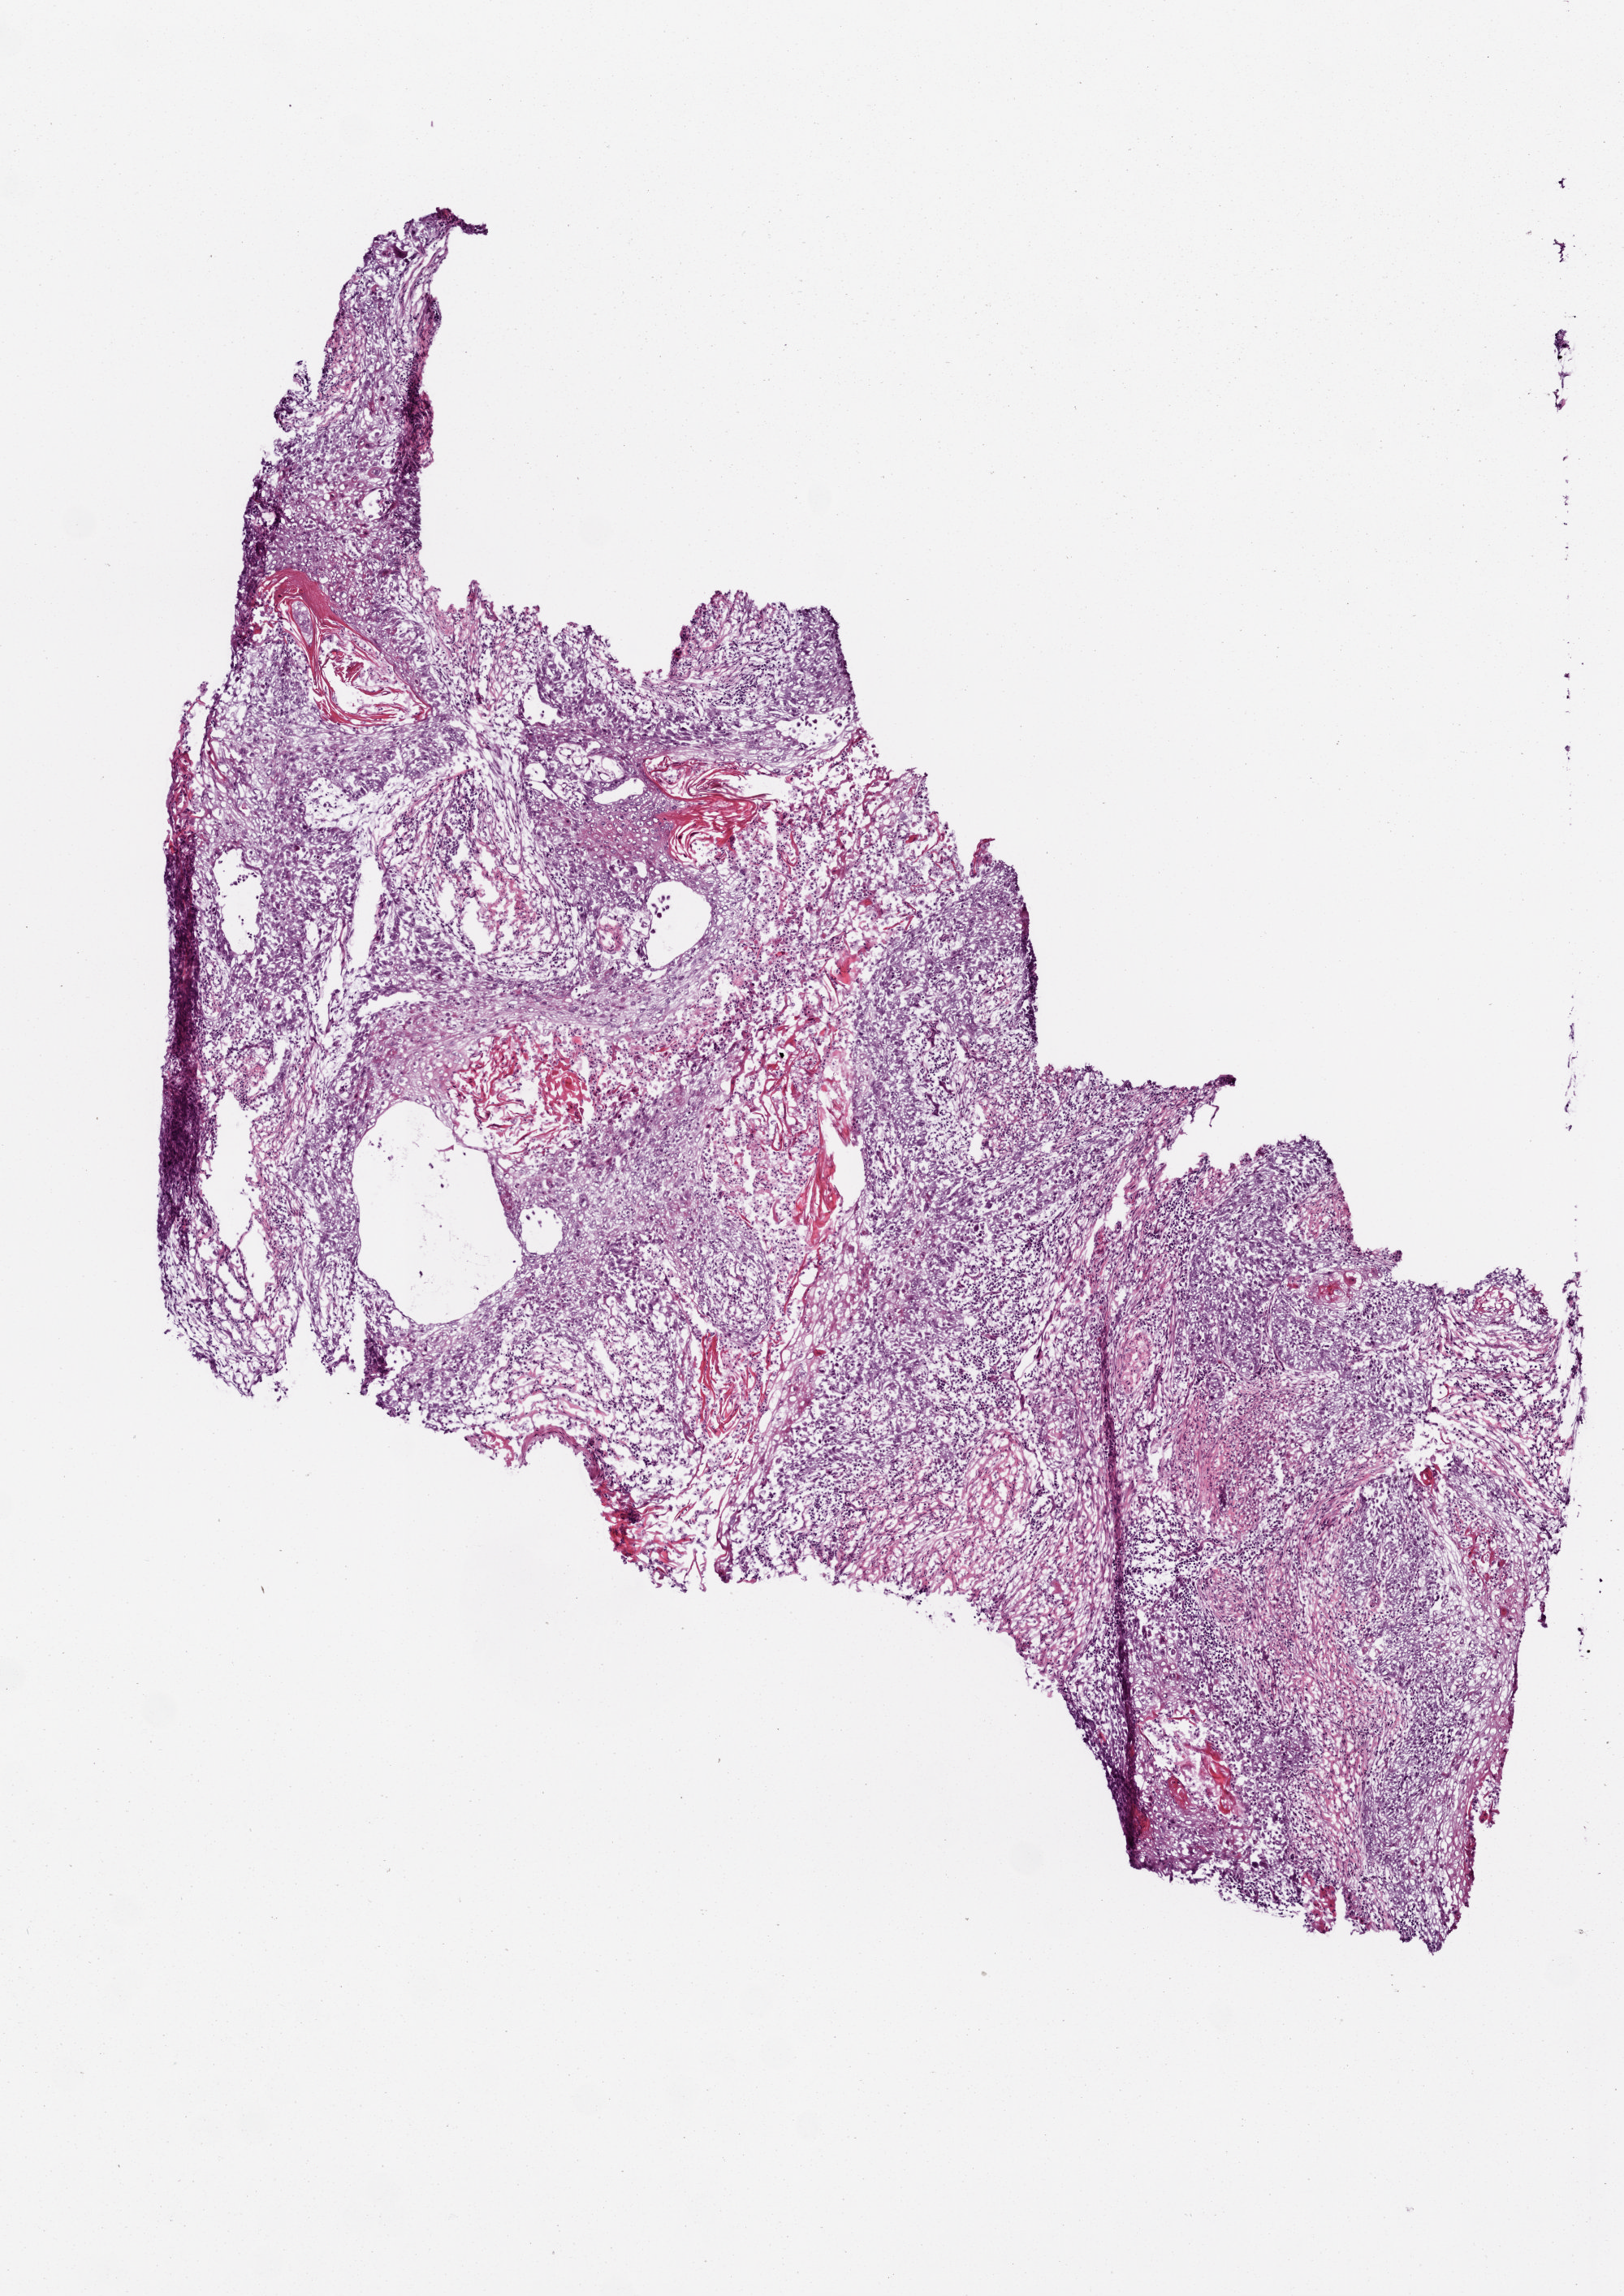
Whole-slide histology image, H&E, whole scanned area (about 4.0 x 5.7 mm, slide scanned at 20x) shown as a low-resolution overview. Frozen section from the top of the tissue portion. Sample: primary tumour, head and neck. Patient: male, age at initial diagnosis 59 years. Histologic grade: G2 (moderately differentiated). Composition of this section per pathologist review: tumour cells 90%, tumour nuclei 80%, normal cells 0%, stromal cells 10%, necrosis 0%.
Pathologic diagnosis: Squamous cell carcinoma, NOS. AJCC pathologic stage: IVA (6th edition).